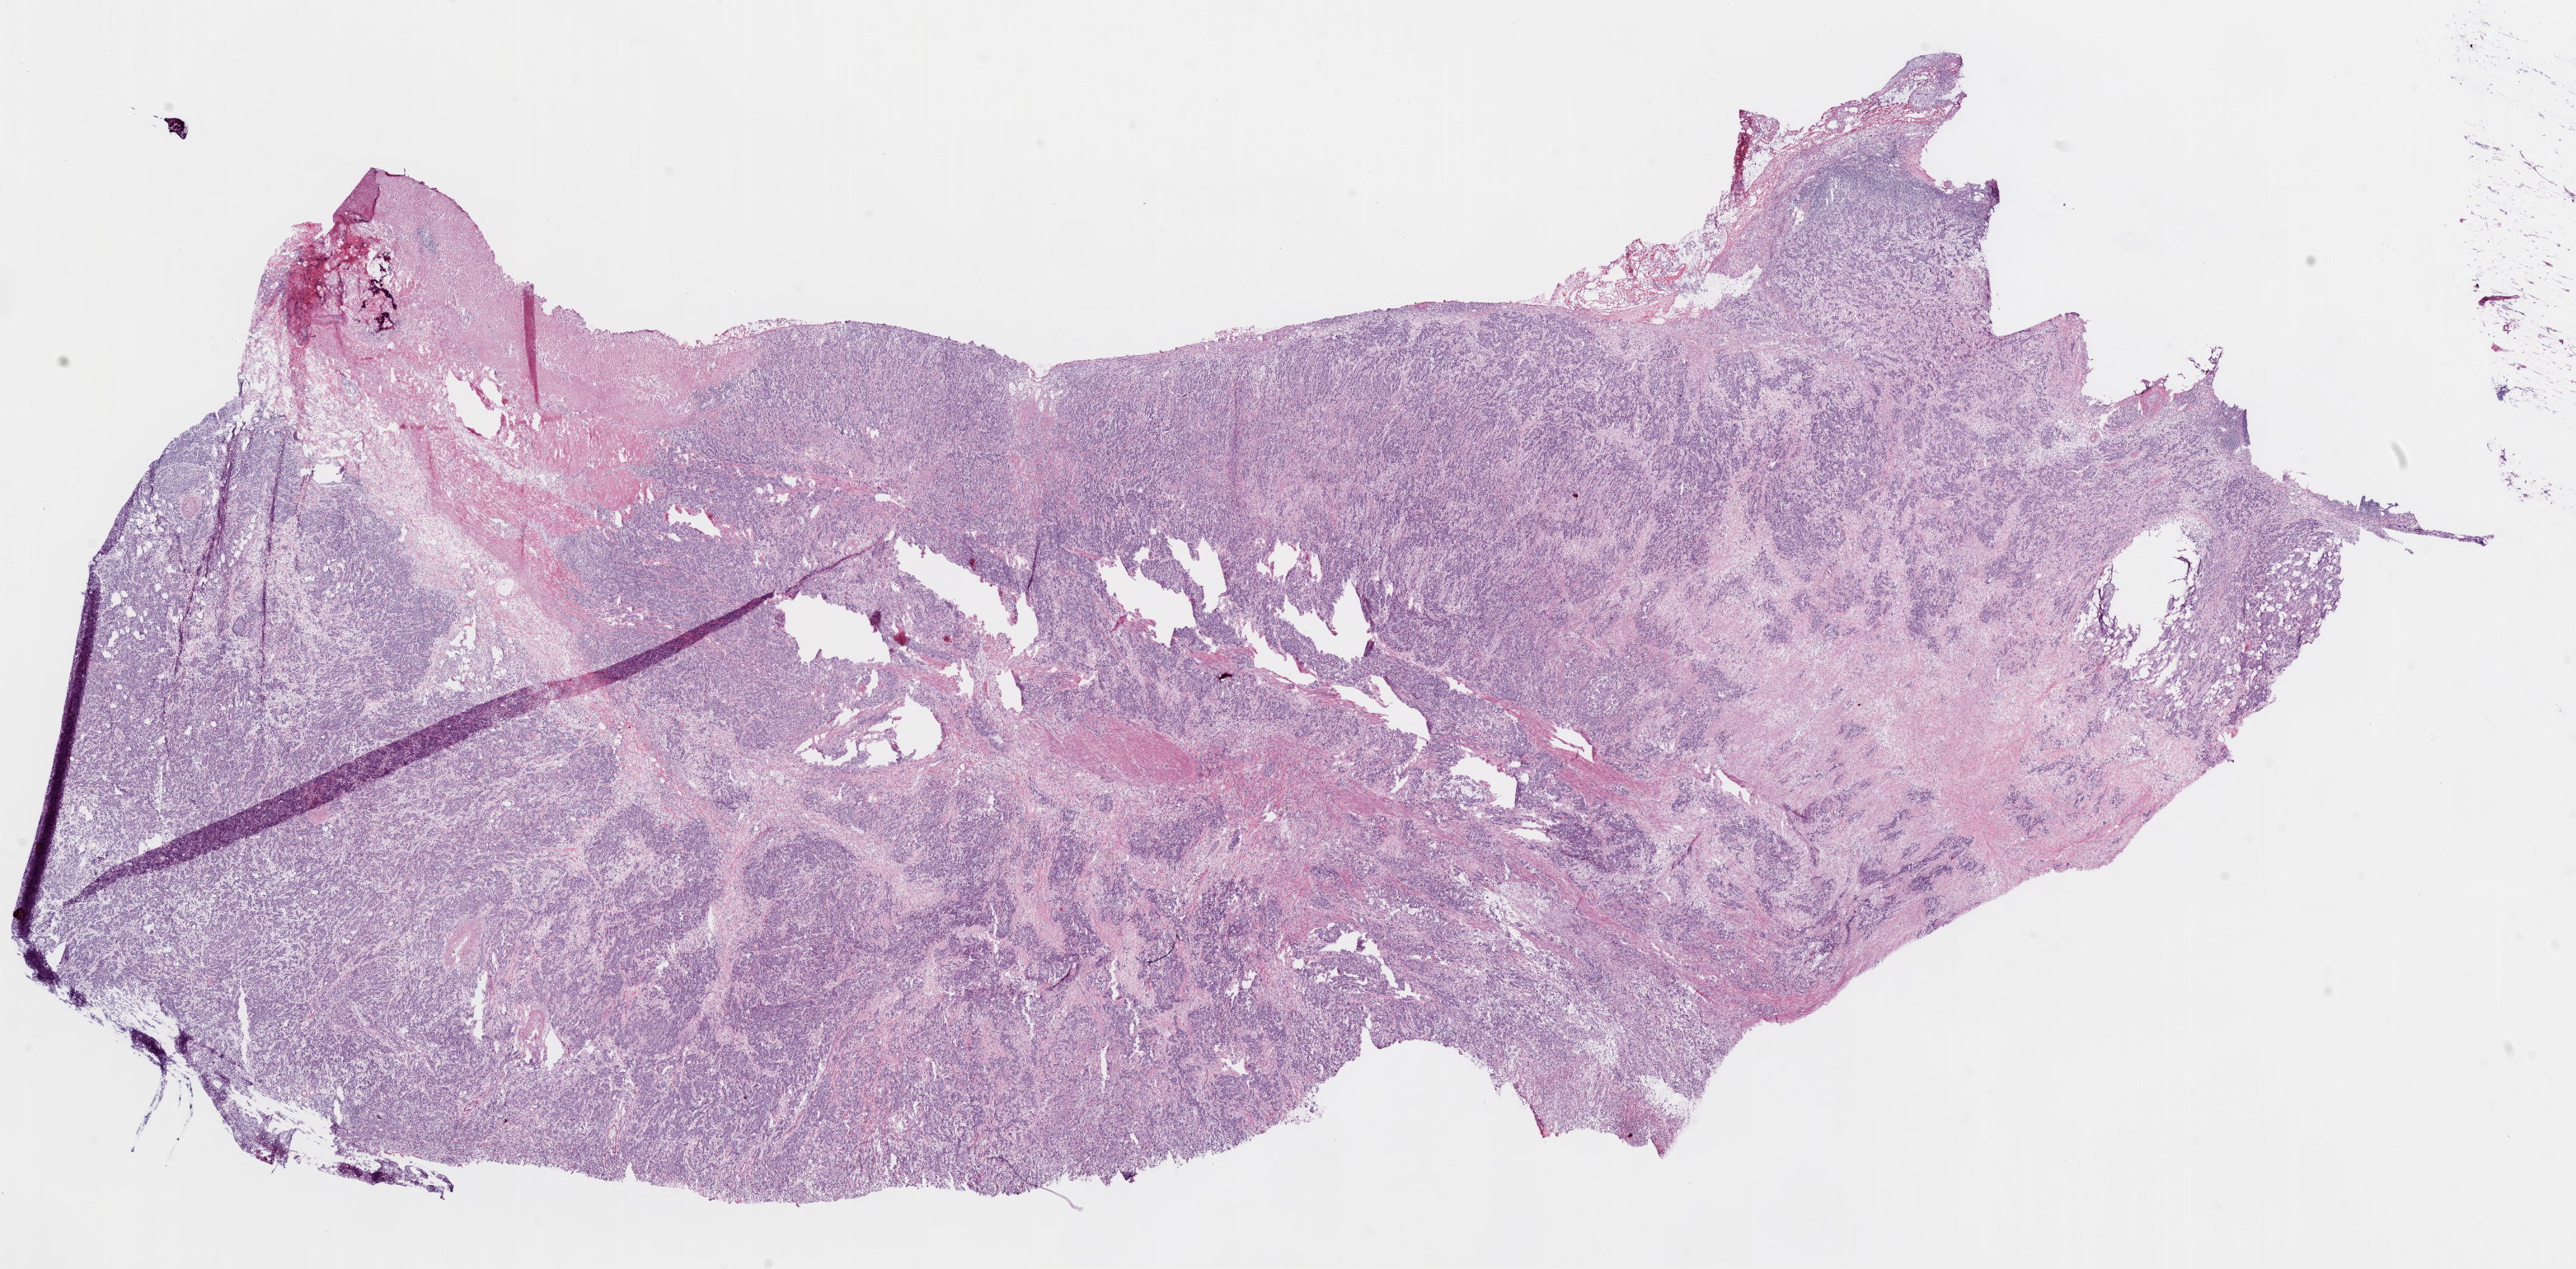
H&E-stained whole-slide image — whole scanned area (about 25.1 x 12.4 mm, acquisition: 20x scan) shown as a low-resolution overview; frozen section; stomach, primary tumour sample. Female, age 66 years at initial diagnosis. Histologic grade: G3 (poorly differentiated). Pathologist review of this section (percent, as recorded): tumour cells 70%, tumour nuclei 80%, normal cells 5%, stromal cells 18%, necrosis 3%.
AJCC pathologic stage: IIIA (6th edition). Lymph nodes positive (case pathology): 0 of 8 examined. TNM: T4 N0 M0. Histologic diagnosis: Adenocarcinoma, NOS.